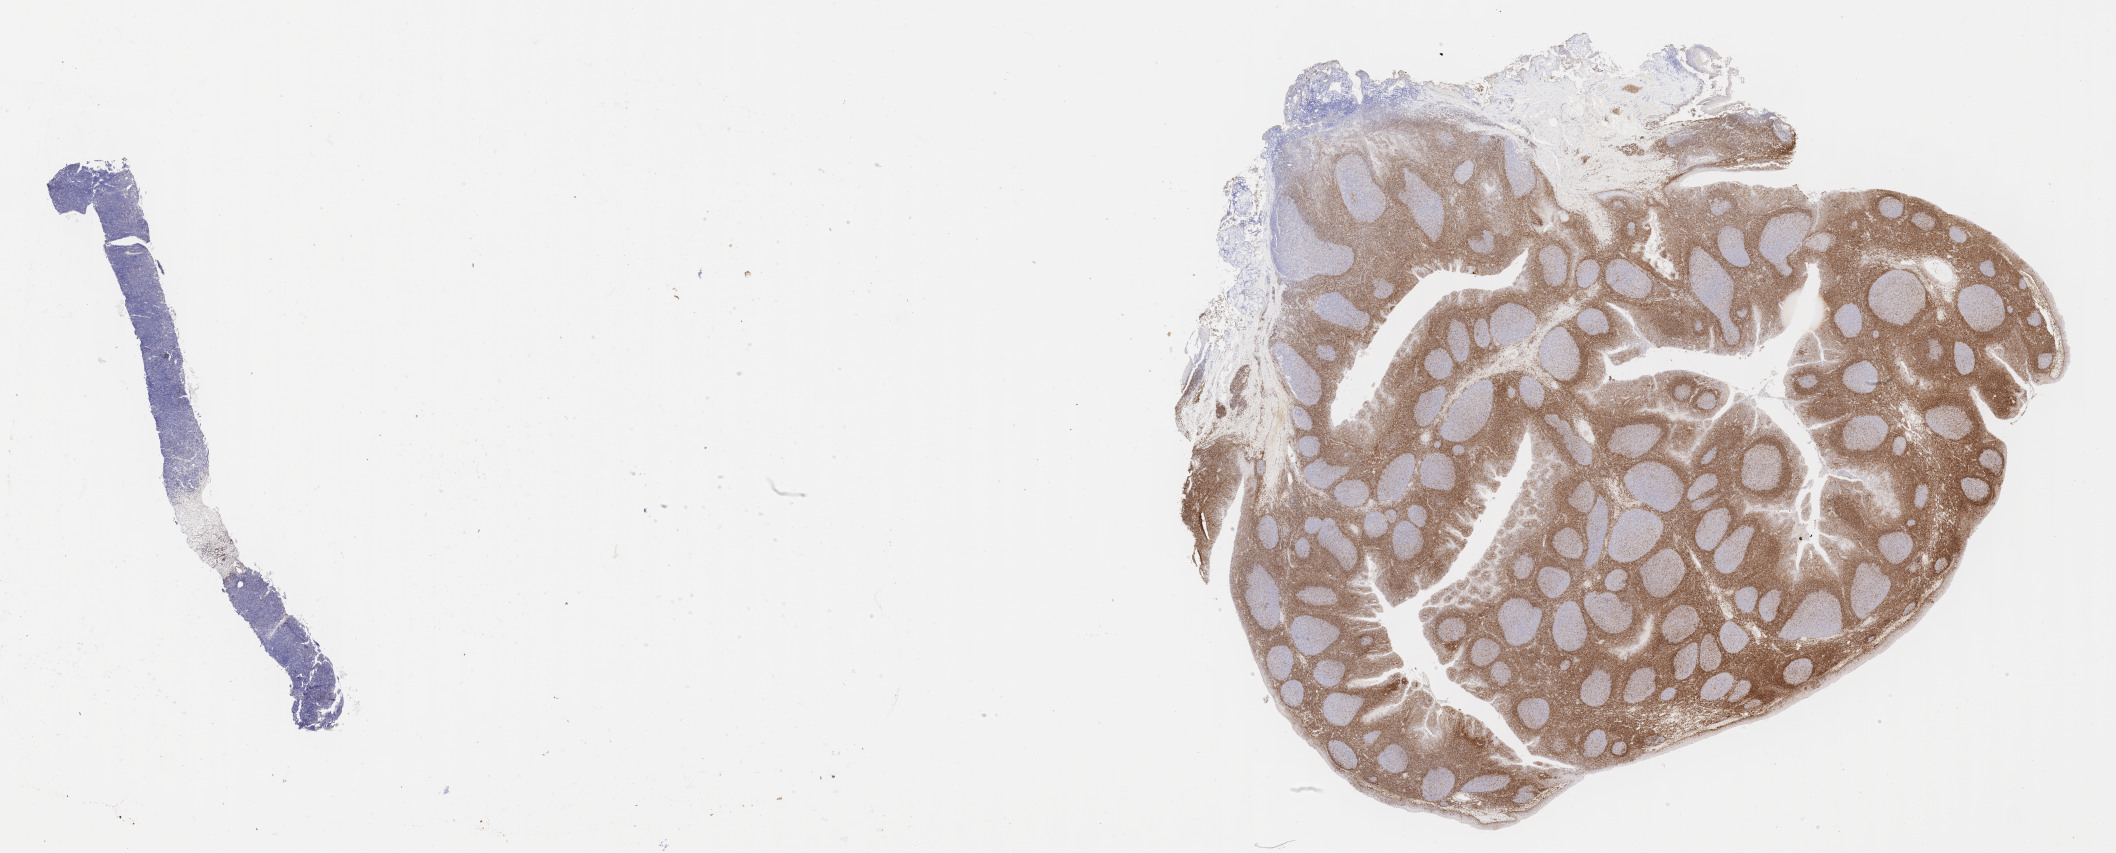
Immunohistochemistry (IHC) whole-slide image stained for BCL2, shown as a low-resolution overview of the whole scanned area (about 34.2 x 13.8 mm), specimen: tumor tissue. Male patient; age at initial diagnosis 7 years.
Histologic diagnosis: Neoplasm, uncertain whether benign or malignant.